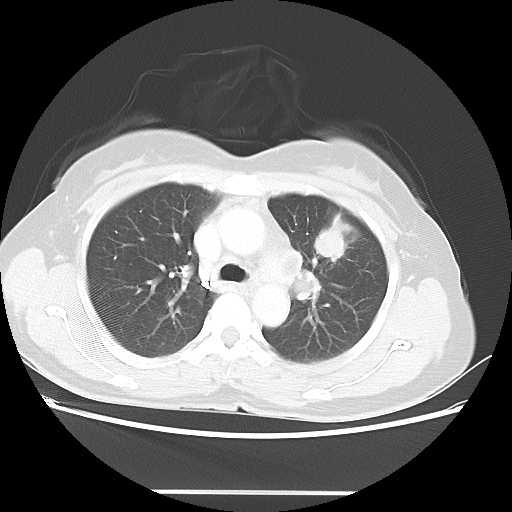
Chest CT, one axial slice. Slice 32 of 46 in the series (ordered by position). Lung window (W 1500 / L -600 HU). 512 × 512 image matrix, field of view 360 × 360 mm. Patient: female, 50 years. Case-level facts recorded for this patient, not image findings: clinical TNM (as recorded): T1c N1 M0; histopathological grade: G3.
Structures marked on this image (rectangle marked by the reading radiologist):
- lung tumour (recorded histology: adenocarcinoma): bounding box <310,211,350,264> (left, top, right, bottom; pixels)